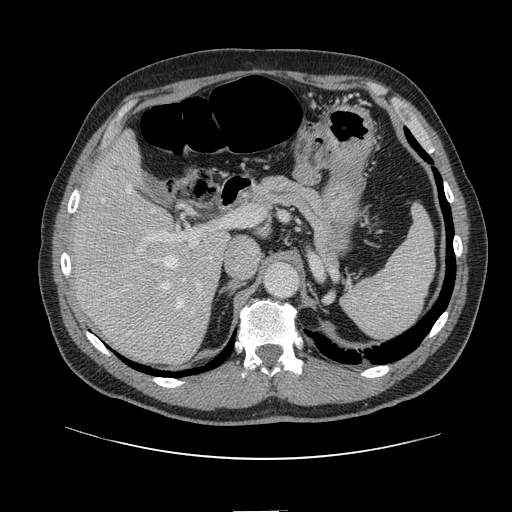
Contrast-enhanced abdominal CT, one axial slice; slice 86 of 161 in the series (ordered by position); 120 kVp; soft-tissue window (W 400 / L 40 HU); 2.5 mm slice thickness; 512 × 512 image matrix. Male patient, age 66 years. From the clinical record (not read from this slice): diagnosis: colorectal cancer liver metastases, imaged before liver resection; multiple liver metastases: no; largest metastasis: 3.5 cm; chemotherapy before resection: yes.
Outlined on this slice (outlined manually by an expert reader):
- hepatic veins: bounding box [x1, y1, x2, y2] px = [102, 185, 185, 335]
- liver: [75, 137, 226, 362]
- planned liver remnant (the part of the liver to remain after resection): [75, 136, 169, 303]
- portal vein (with intrahepatic branches): [129, 217, 250, 314]
- liver metastasis: [114, 166, 120, 172]